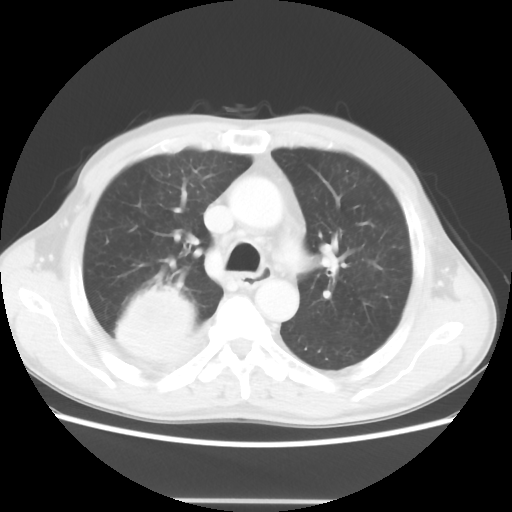
Chest CT, one axial slice. Position 34 of 48 along the scan axis. Reconstruction kernel STANDARD. Lung window (W 1500 / L -600 HU). 5 mm slice thickness. 512 × 512 image matrix, field of view 361 × 361 mm. Patient: male, 66 years. Case-level facts recorded for this patient, not image findings: clinical TNM (as recorded): T4 N1 M1; histopathological grade: G3.
Outlined on this slice (bounding box drawn by a radiologist):
- lung tumour (recorded histology: small cell carcinoma): bounding box (x1, y1, x2, y2) in pixels: (104, 280, 204, 376)